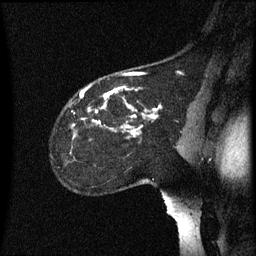
Breast MRI (dynamic contrast-enhanced), one sagittal slice. Slice 44 of 60 in the series (ordered by position). Dynamic contrast-enhanced series, image 2 of 3 at this slice position (ordered by acquisition). 1.5 T. TE 4.2 ms, TR 8.4 ms. 256 × 256 image matrix. Female patient, age 35 years. From the clinical record (not read from this slice): setting: breast cancer imaged before/during neoadjuvant chemotherapy; receptor status: HER2-positive.
Outlined on this slice (semi-automatic segmentation, software-assisted and operator-edited):
- analysis volume of interest (the breast-tissue region the enhancement analysis was run in; not a lesion): box from (x=52, y=72) to (x=174, y=169) px
- tumour enhancement mask (voxels above the 70 % enhancement threshold inside the analysis volume of interest): (x=72, y=88)–(x=159, y=137)